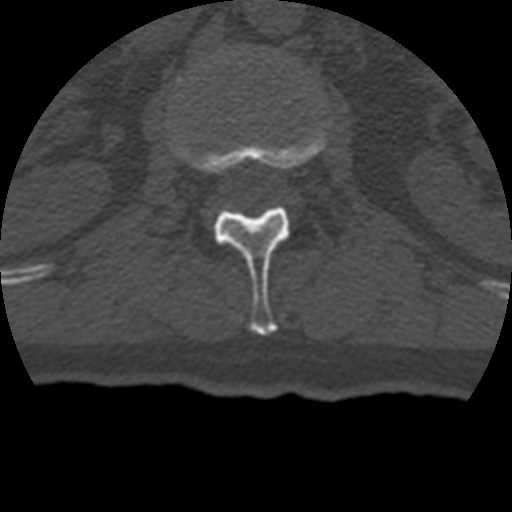
CT including the spine, one axial slice. Position 137 of 399 along the scan axis. Reconstruction kernel STANDARD. Bone window (W 1800 / L 400 HU). 1.25 mm slice thickness. 512 × 512 image matrix, field of view 160 × 160 mm. Patient age 69 years. From the clinical record (not read from this slice): primary cancer: prostate.
Annotated regions visible in this slice (semi-automatically segmented with operator editing):
- L1 vertebra: bounding box <173,135,326,335> (left, top, right, bottom; pixels)
- L2 vertebra: <221,50,231,57>